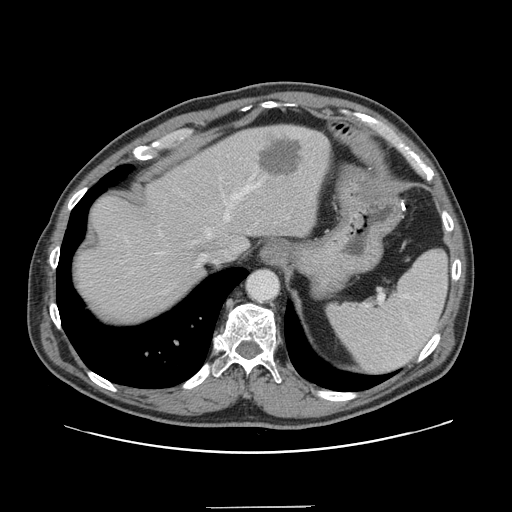
Contrast-enhanced abdominal CT, one axial slice; slice 119 of 139 in the series (ordered by position); intravenous contrast given; soft-tissue window (W 400 / L 40 HU); 2.5 mm slice thickness; 512 × 512 image matrix, field of view 397 × 397 mm. Male patient, age 64 years. From the clinical record (not read from this slice): diagnosis: colorectal cancer liver metastases, imaged before liver resection; multiple liver metastases: yes; largest metastasis: 3.5 cm; chemotherapy before resection: yes.
Structures marked on this image (manually delineated by an expert):
- hepatic veins: box from (x=193, y=183) to (x=260, y=243) px
- liver: (x=75, y=126)–(x=329, y=324)
- planned liver remnant (the part of the liver to remain after resection): (x=75, y=131)–(x=264, y=324)
- liver metastasis: (x=260, y=141)–(x=302, y=176)